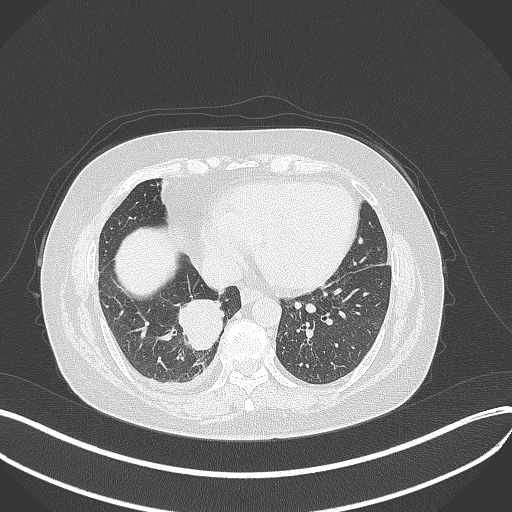
Chest CT, one axial slice. Position 120 of 381 along the scan axis. Lung window (W 1500 / L -600 HU). 1 mm slice thickness. 512 × 512 image matrix, field of view 400 × 400 mm. Patient: female, 56 years. From the clinical record (not read from this slice): clinical TNM (as recorded): T2b N1 M0; histopathological grade: G3.
Structures marked on this image (rectangle marked by the reading radiologist):
- lung tumour (recorded histology: small cell carcinoma): bounding box (x1, y1, x2, y2) in pixels: (175, 299, 224, 353)